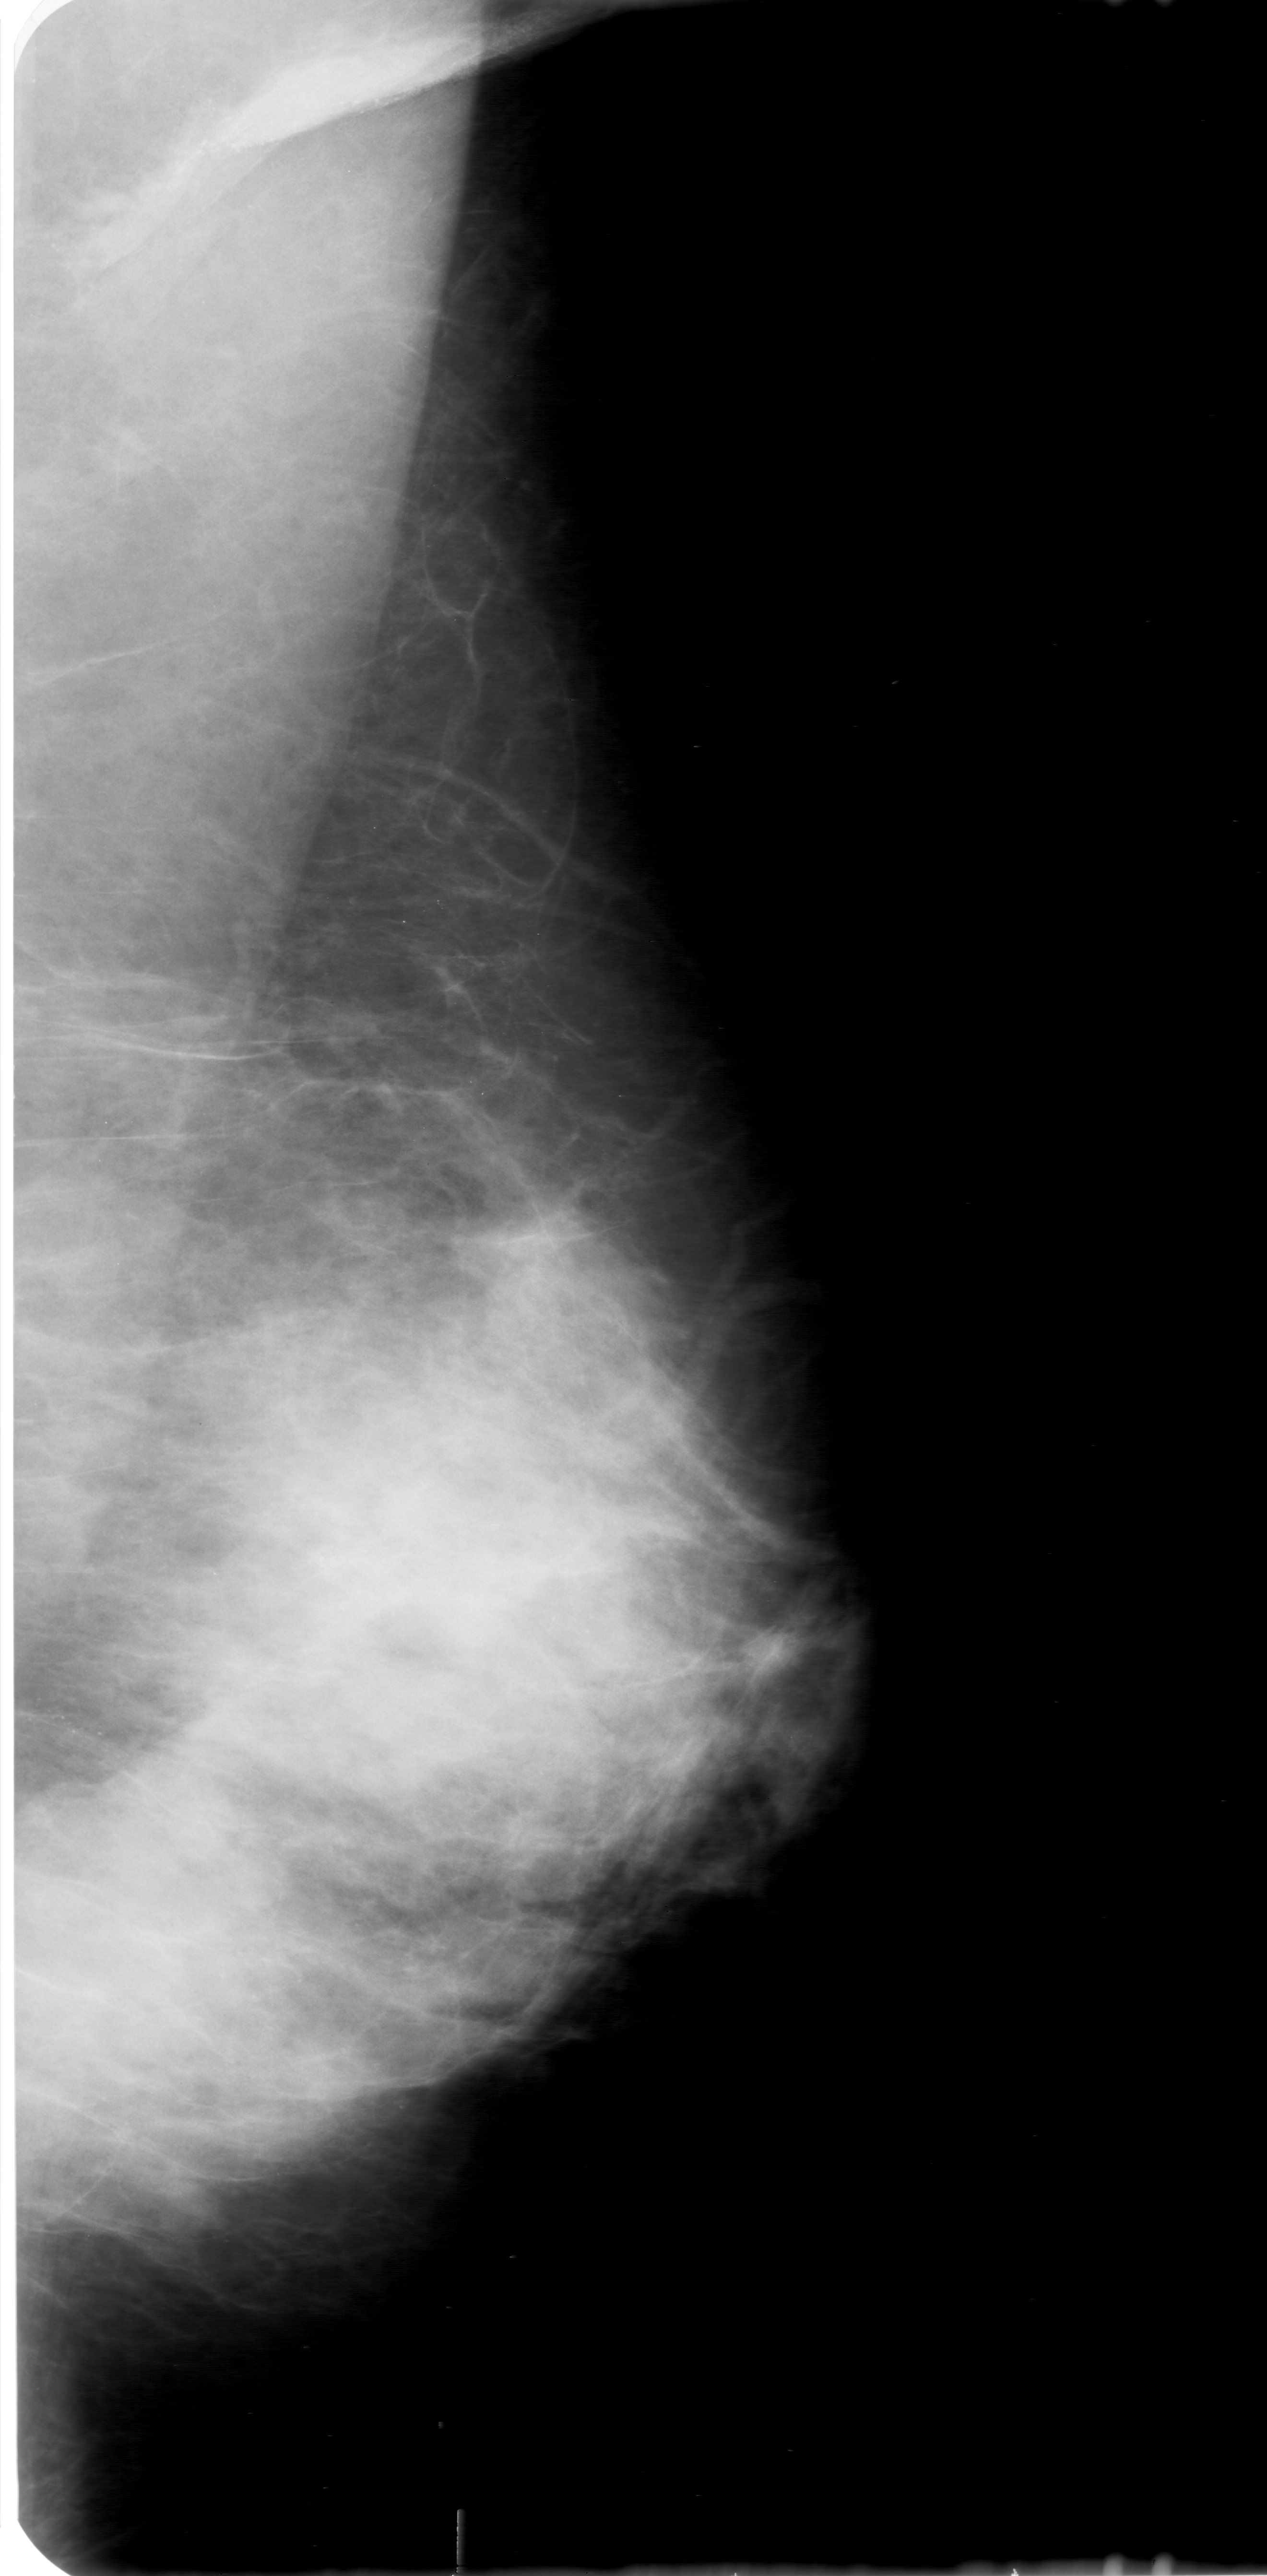
Mammogram (digitized film); left breast; MLO view; 1267 × 2576 image matrix.
Expert-marked regions of interest on this film, with their recorded descriptors:
- calcifications, morphology pleomorphic, distribution clustered; BI-RADS assessment category 0; pathology (as recorded): malignant: box from (x=22, y=1628) to (x=165, y=1810) px